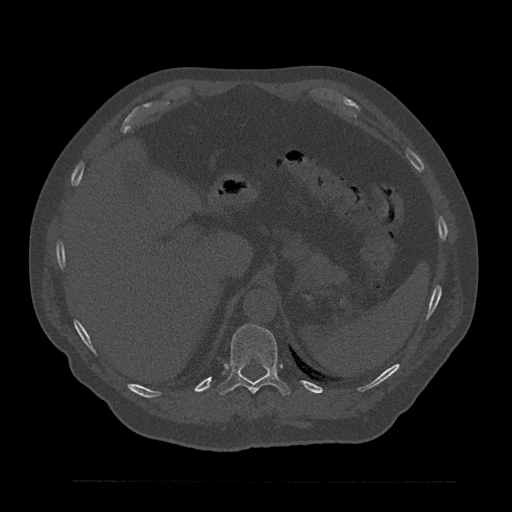
CT including the spine, one axial slice; position 297 of 797 along the scan axis; reconstruction kernel Br40s/3; bone window (W 1800 / L 400 HU); 0.5 mm slice thickness; 512 × 512 image matrix, field of view 430 × 430 mm. Patient: male, 61 years. Case-level facts recorded for this patient, not image findings: primary cancer: prostate.
Outlined on this slice (semi-automatically segmented with operator editing):
- T11 vertebra: bounding box (x1, y1, x2, y2) in pixels: (217, 324, 290, 395)